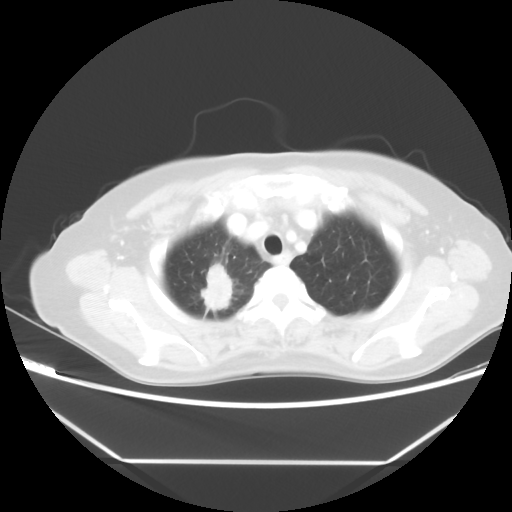
Chest CT, one axial slice; slice 42 of 48 in the series (ordered by position); reconstruction kernel STANDARD; lung window (W 1500 / L -600 HU); 5 mm slice thickness; 512 × 512 image matrix, field of view 360 × 360 mm. Female patient, age 65 years. From the clinical record (not read from this slice): clinical TNM (as recorded): T1c N1 M1.
Outlined on this slice (bounding box drawn by a radiologist):
- lung tumour (recorded histology: adenocarcinoma): box from (x=201, y=262) to (x=237, y=310) px